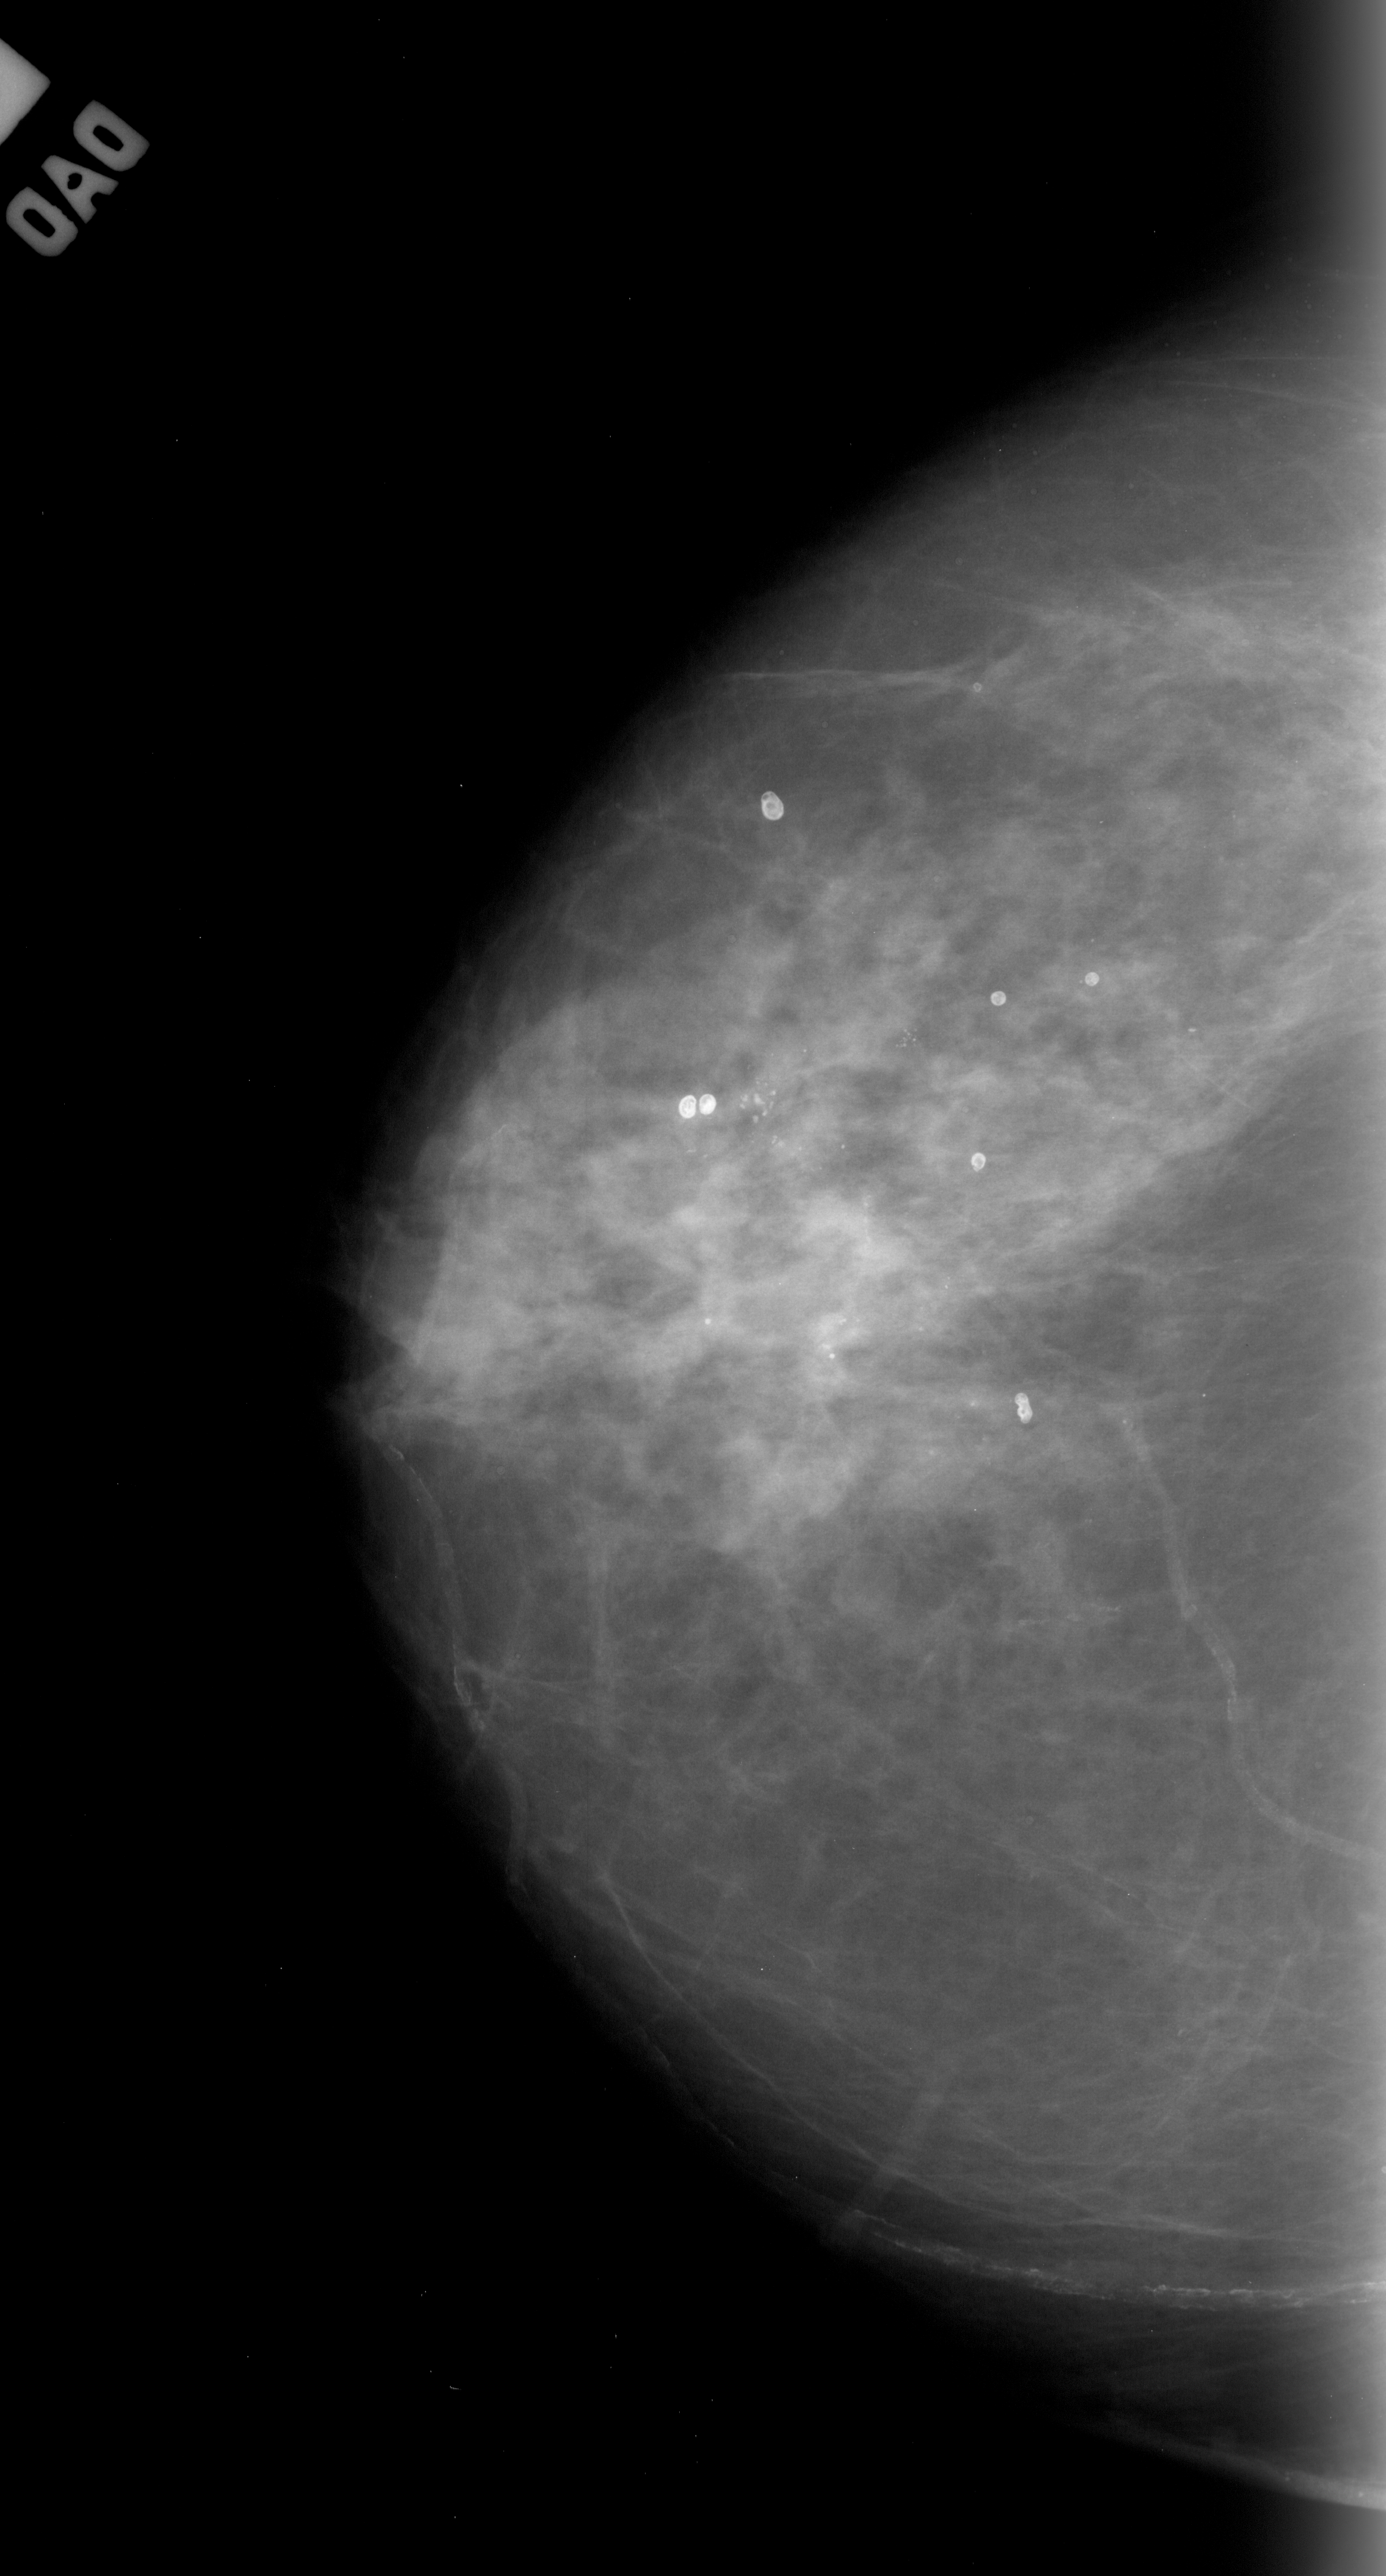
Digitized screen-film mammogram, left breast, CC view, breast composition: heterogeneously dense (BI-RADS density category 3 of 4).
- Radiologist-marked abnormalities on this image: calcifications, morphology pleomorphic, distribution segmental; BI-RADS assessment category 4; pathology (as recorded): malignant.